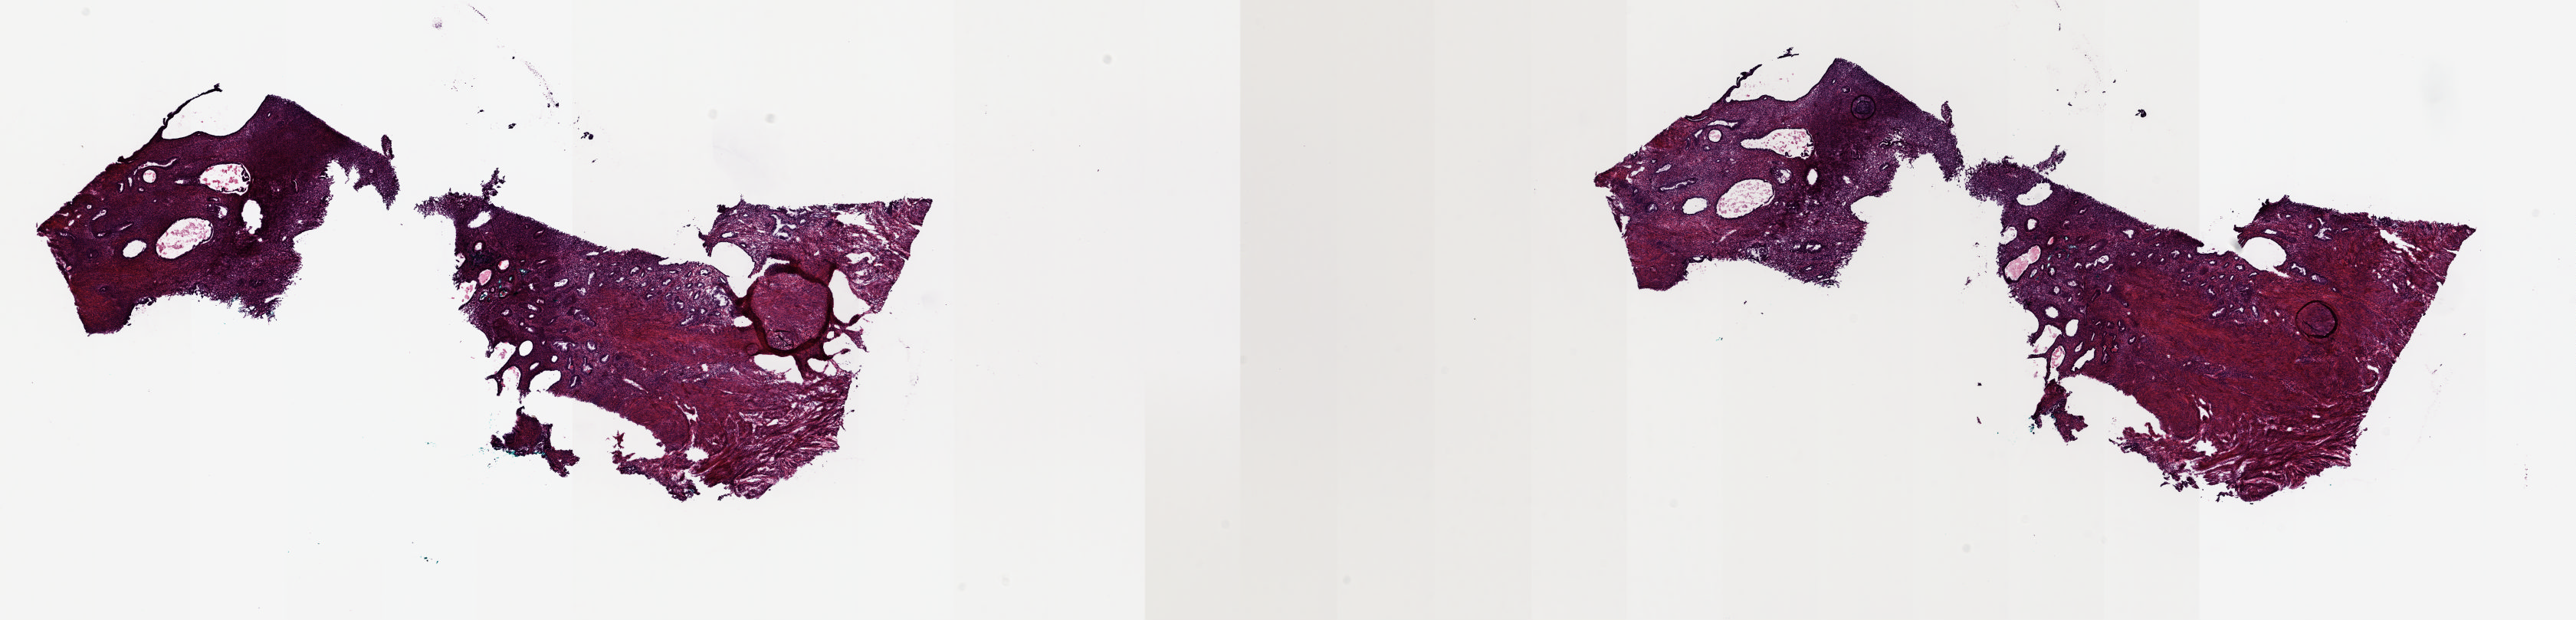
Whole-slide histology image, H&E, shown as a low-resolution overview of the whole scanned area (about 26.7 x 6.4 mm). Frozen section. Solid tissue normal (non-tumour tissue) sample from the uterus. Pathologist review of this section (percent, as recorded): tumour cells 0%, normal cells 100%.
* this section: solid tissue normal sample (biorepository sample class)